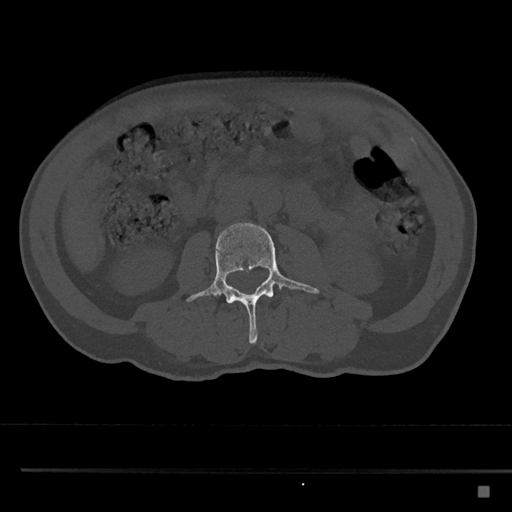
CT including the spine, one axial slice. Position 697 of 797 along the scan axis. Reconstruction kernel Br40s/3. 120 kVp. Bone window (W 1800 / L 400 HU). 0.5 mm slice thickness. 512 × 512 image matrix, field of view 391 × 391 mm. Male patient, age 59 years. From the clinical record (not read from this slice): primary cancer: prostate.
Outlined on this slice (semi-automatic segmentation, software-assisted and operator-edited):
- L3 vertebra: bounding box [x1, y1, x2, y2] px = [187, 223, 319, 345]